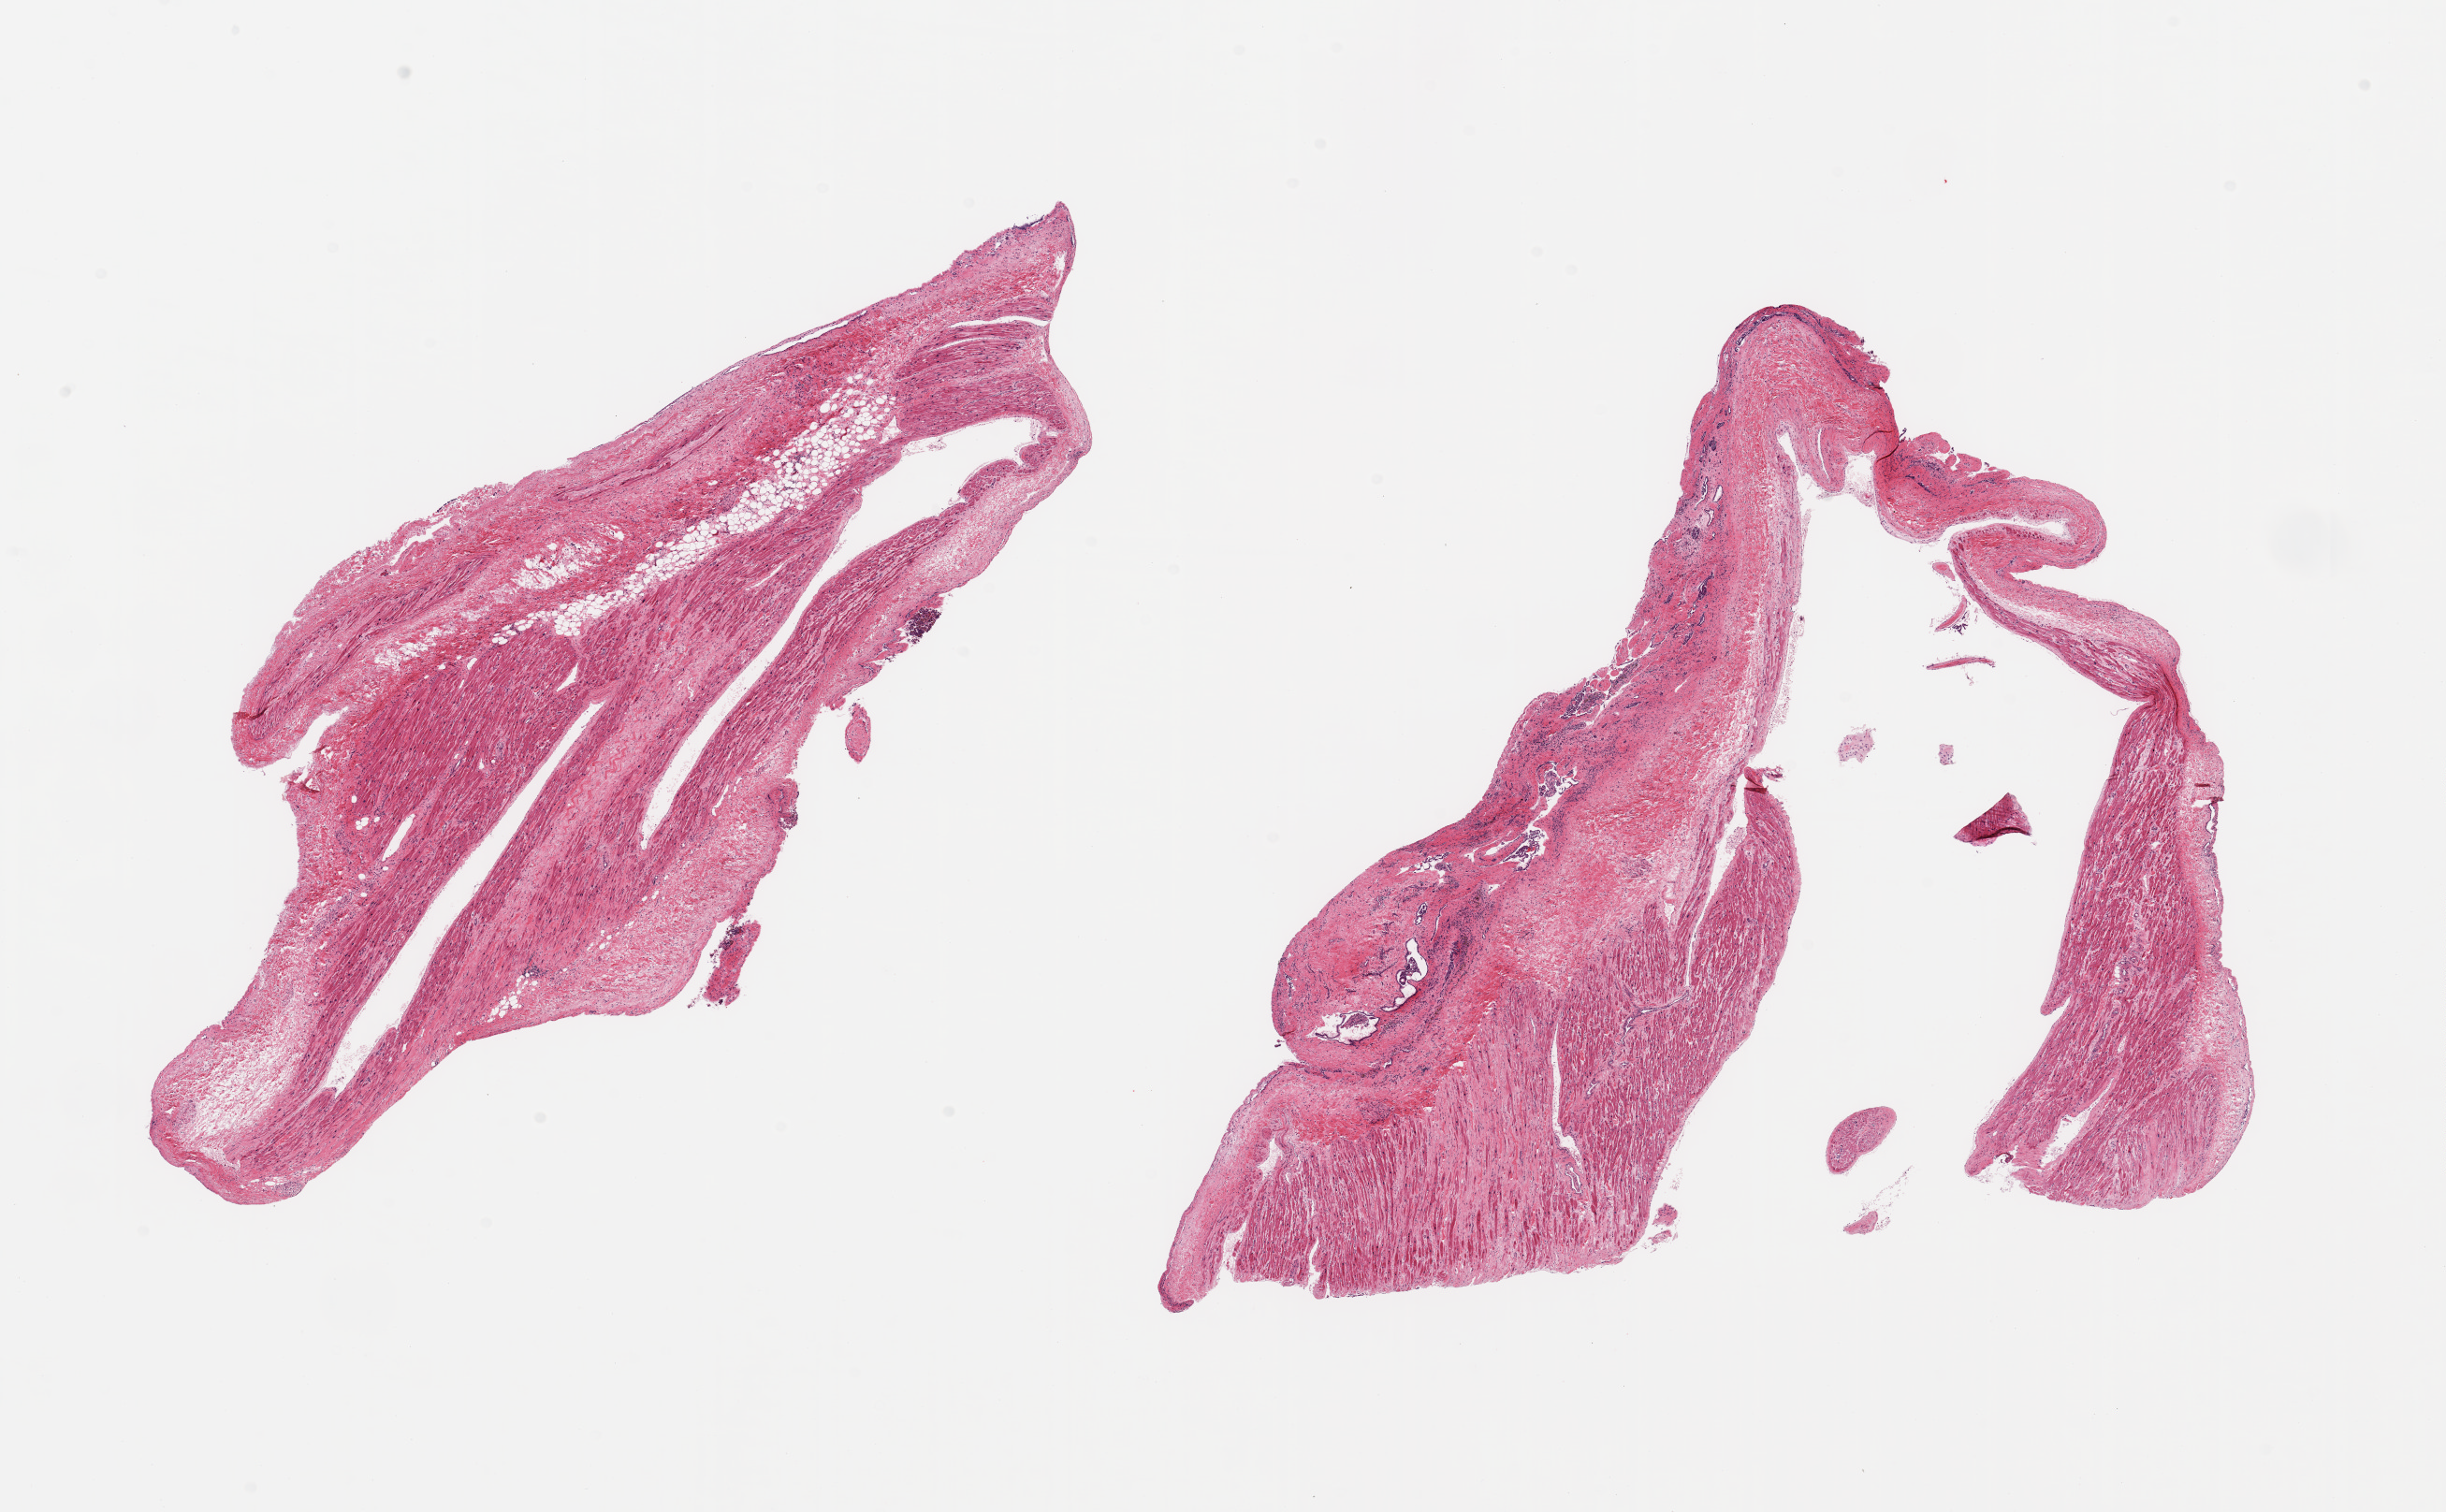
Whole-slide image, hematoxylin and eosin (H&E) stain — a low-resolution overview of the entire scanned area, about 20.7 x 12.8 mm, PAXgene-fixed paraffin-embedded (PFPE) section, section of auricular appendage (target tissue), donor tissue sample. Donor sex: male.
* reviewer comment on this tissue sample: 2 pieces; 50% fibrous & fatty content